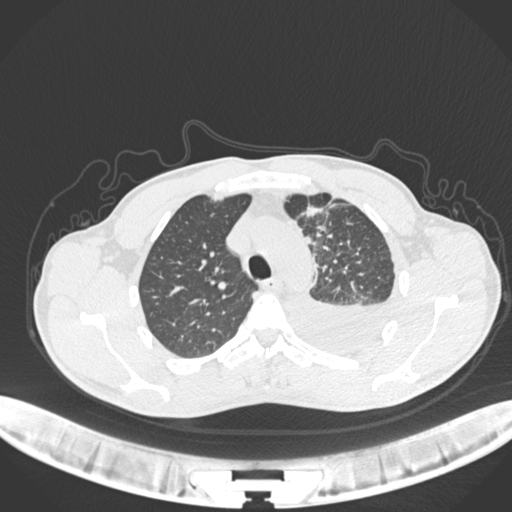
Chest CT, one axial slice. Slice 169 of 244 in the series (ordered by position). Reconstruction kernel B30f. Lung window (W 1500 / L -600 HU). 1 mm slice thickness. 512 × 512 image matrix. Patient: male, 49 years. Case-level facts recorded for this patient, not image findings: clinical TNM (as recorded): T1c N1 M1.
Structures marked on this image (bounding box drawn by a radiologist):
- lung tumour (recorded histology: adenocarcinoma): box from (x=300, y=199) to (x=330, y=225) px